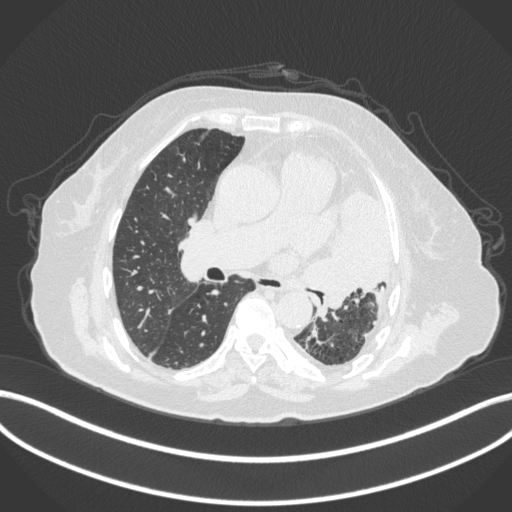
Chest CT, one axial slice; slice 204 of 399 in the series (ordered by position); reconstruction kernel B31f; 120 kVp; lung window (W 1500 / L -600 HU); 1 mm slice thickness; 512 × 512 image matrix, field of view 400 × 400 mm. Female patient, age 75 years. Case-level facts recorded for this patient, not image findings: clinical TNM (as recorded): T3 N3 M1.
Annotated regions visible in this slice (bounding box drawn by a radiologist):
- lung tumour (recorded histology: adenocarcinoma): bounding box (x1, y1, x2, y2) in pixels: (295, 182, 395, 311)